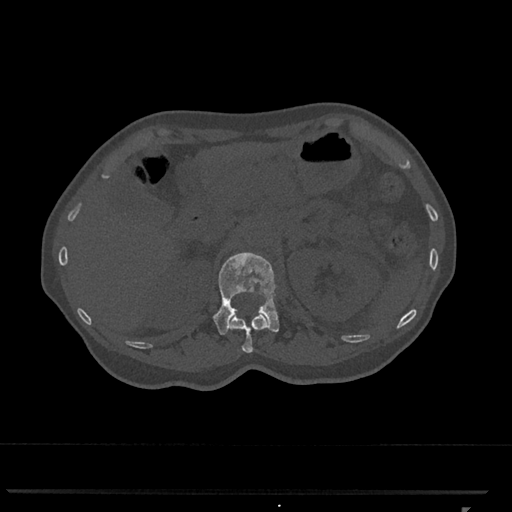
CT including the spine, one axial slice; position 425 of 793 along the scan axis; bone window (W 1800 / L 400 HU); 0.5 mm slice thickness; 512 × 512 image matrix. Patient: female, 62 years. From the clinical record (not read from this slice): primary cancer: renal.
Outlined on this slice (semi-automatic segmentation, software-assisted and operator-edited):
- L1 vertebra: bounding box <212,252,279,335> (left, top, right, bottom; pixels)
- T12 vertebra: <229,312,267,353>